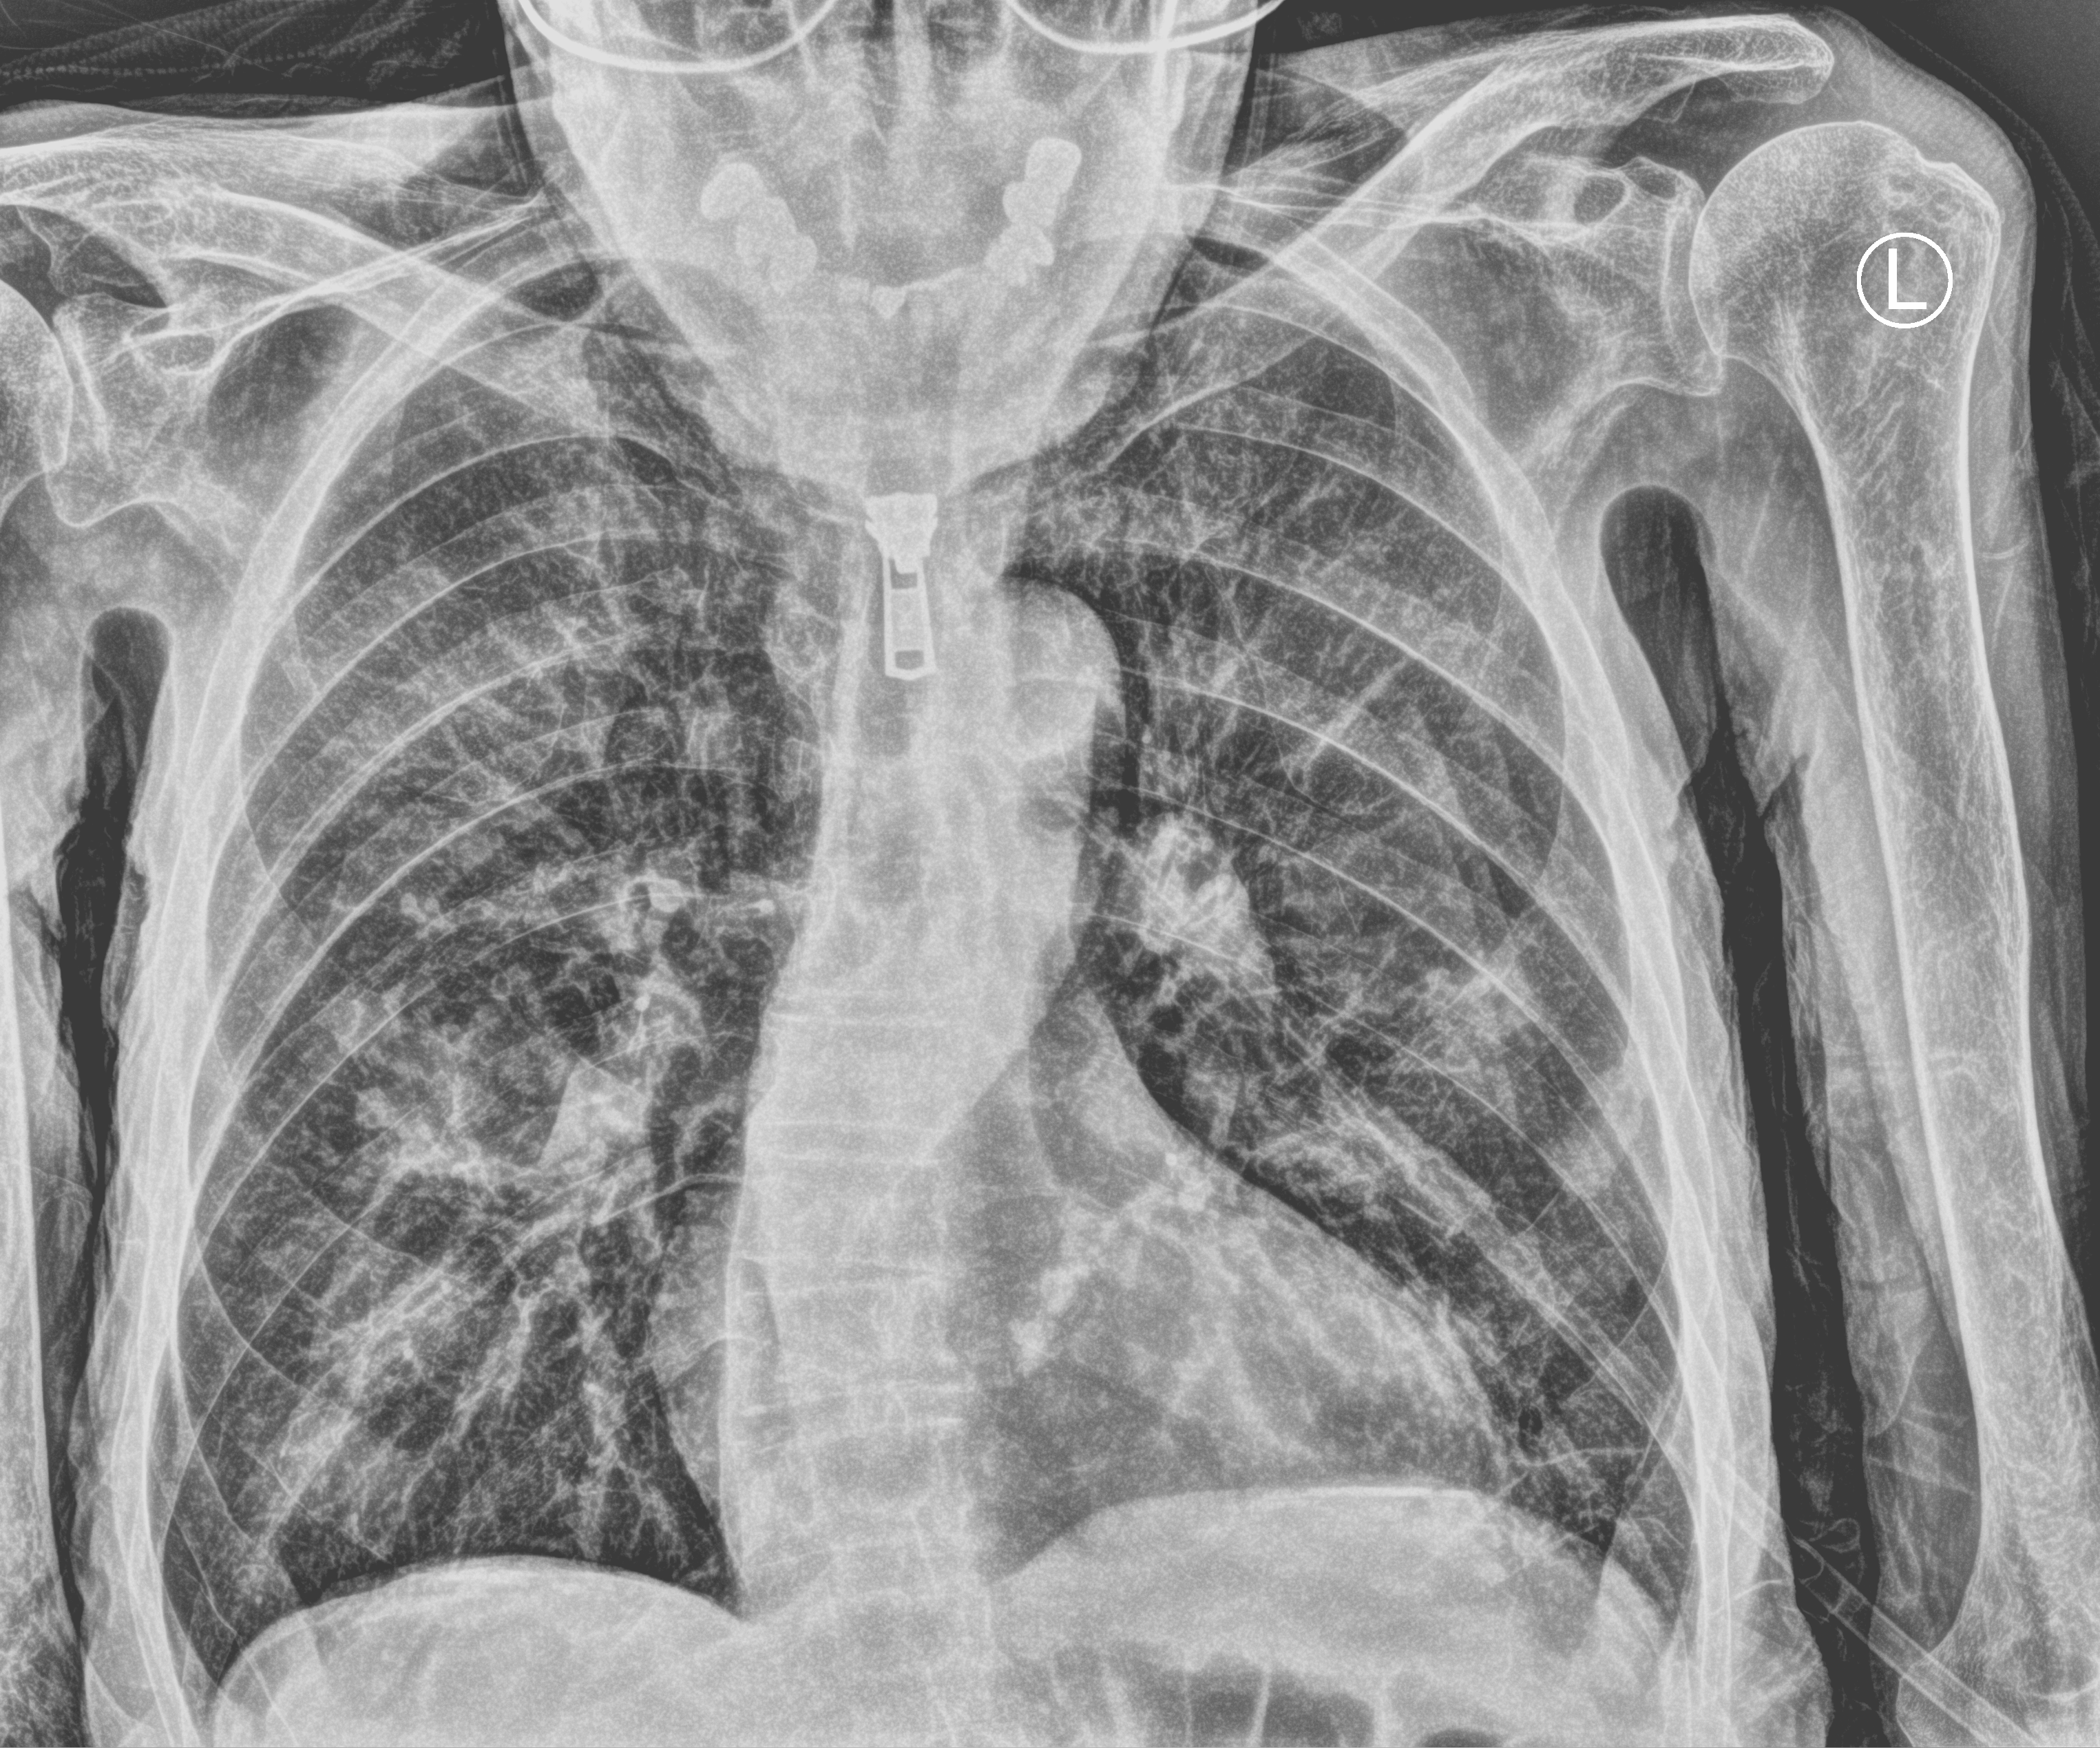
Portable chest radiograph, anteroposterior (AP) projection. Male patient hospitalised with COVID-19, age 75–90 years.
From the hospital-stay record, not from the radiograph (when in the stay this image was taken is not recorded):
- mechanically ventilated during this hospital stay: no
- length of hospital stay: 6 days